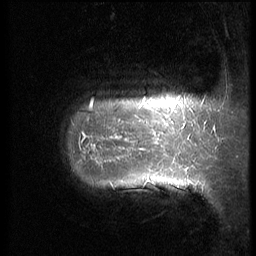
Breast MRI (dynamic contrast-enhanced), one sagittal slice; position 8 of 64 along the scan axis; 3 images stored at this slice position (order not interpretable as contrast timing); 1.5 T; TE 4.2 ms, TR 9 ms; 2.5 mm slice thickness; 256 × 256 image matrix, field of view 180 × 180 mm. Female patient, age 39 years. Case-level facts recorded for this patient, not image findings: setting: breast cancer imaged before/during neoadjuvant chemotherapy; receptor status: HER2-positive.
Outlined on this slice (semi-automatic segmentation, software-assisted and operator-edited):
- analysis volume of interest (the breast-tissue region the enhancement analysis was run in; not a lesion): bounding box (x1, y1, x2, y2) in pixels: (58, 63, 210, 223)
- tumour enhancement mask (voxels above the 140 % enhancement threshold inside the analysis volume of interest): (78, 98, 176, 163)